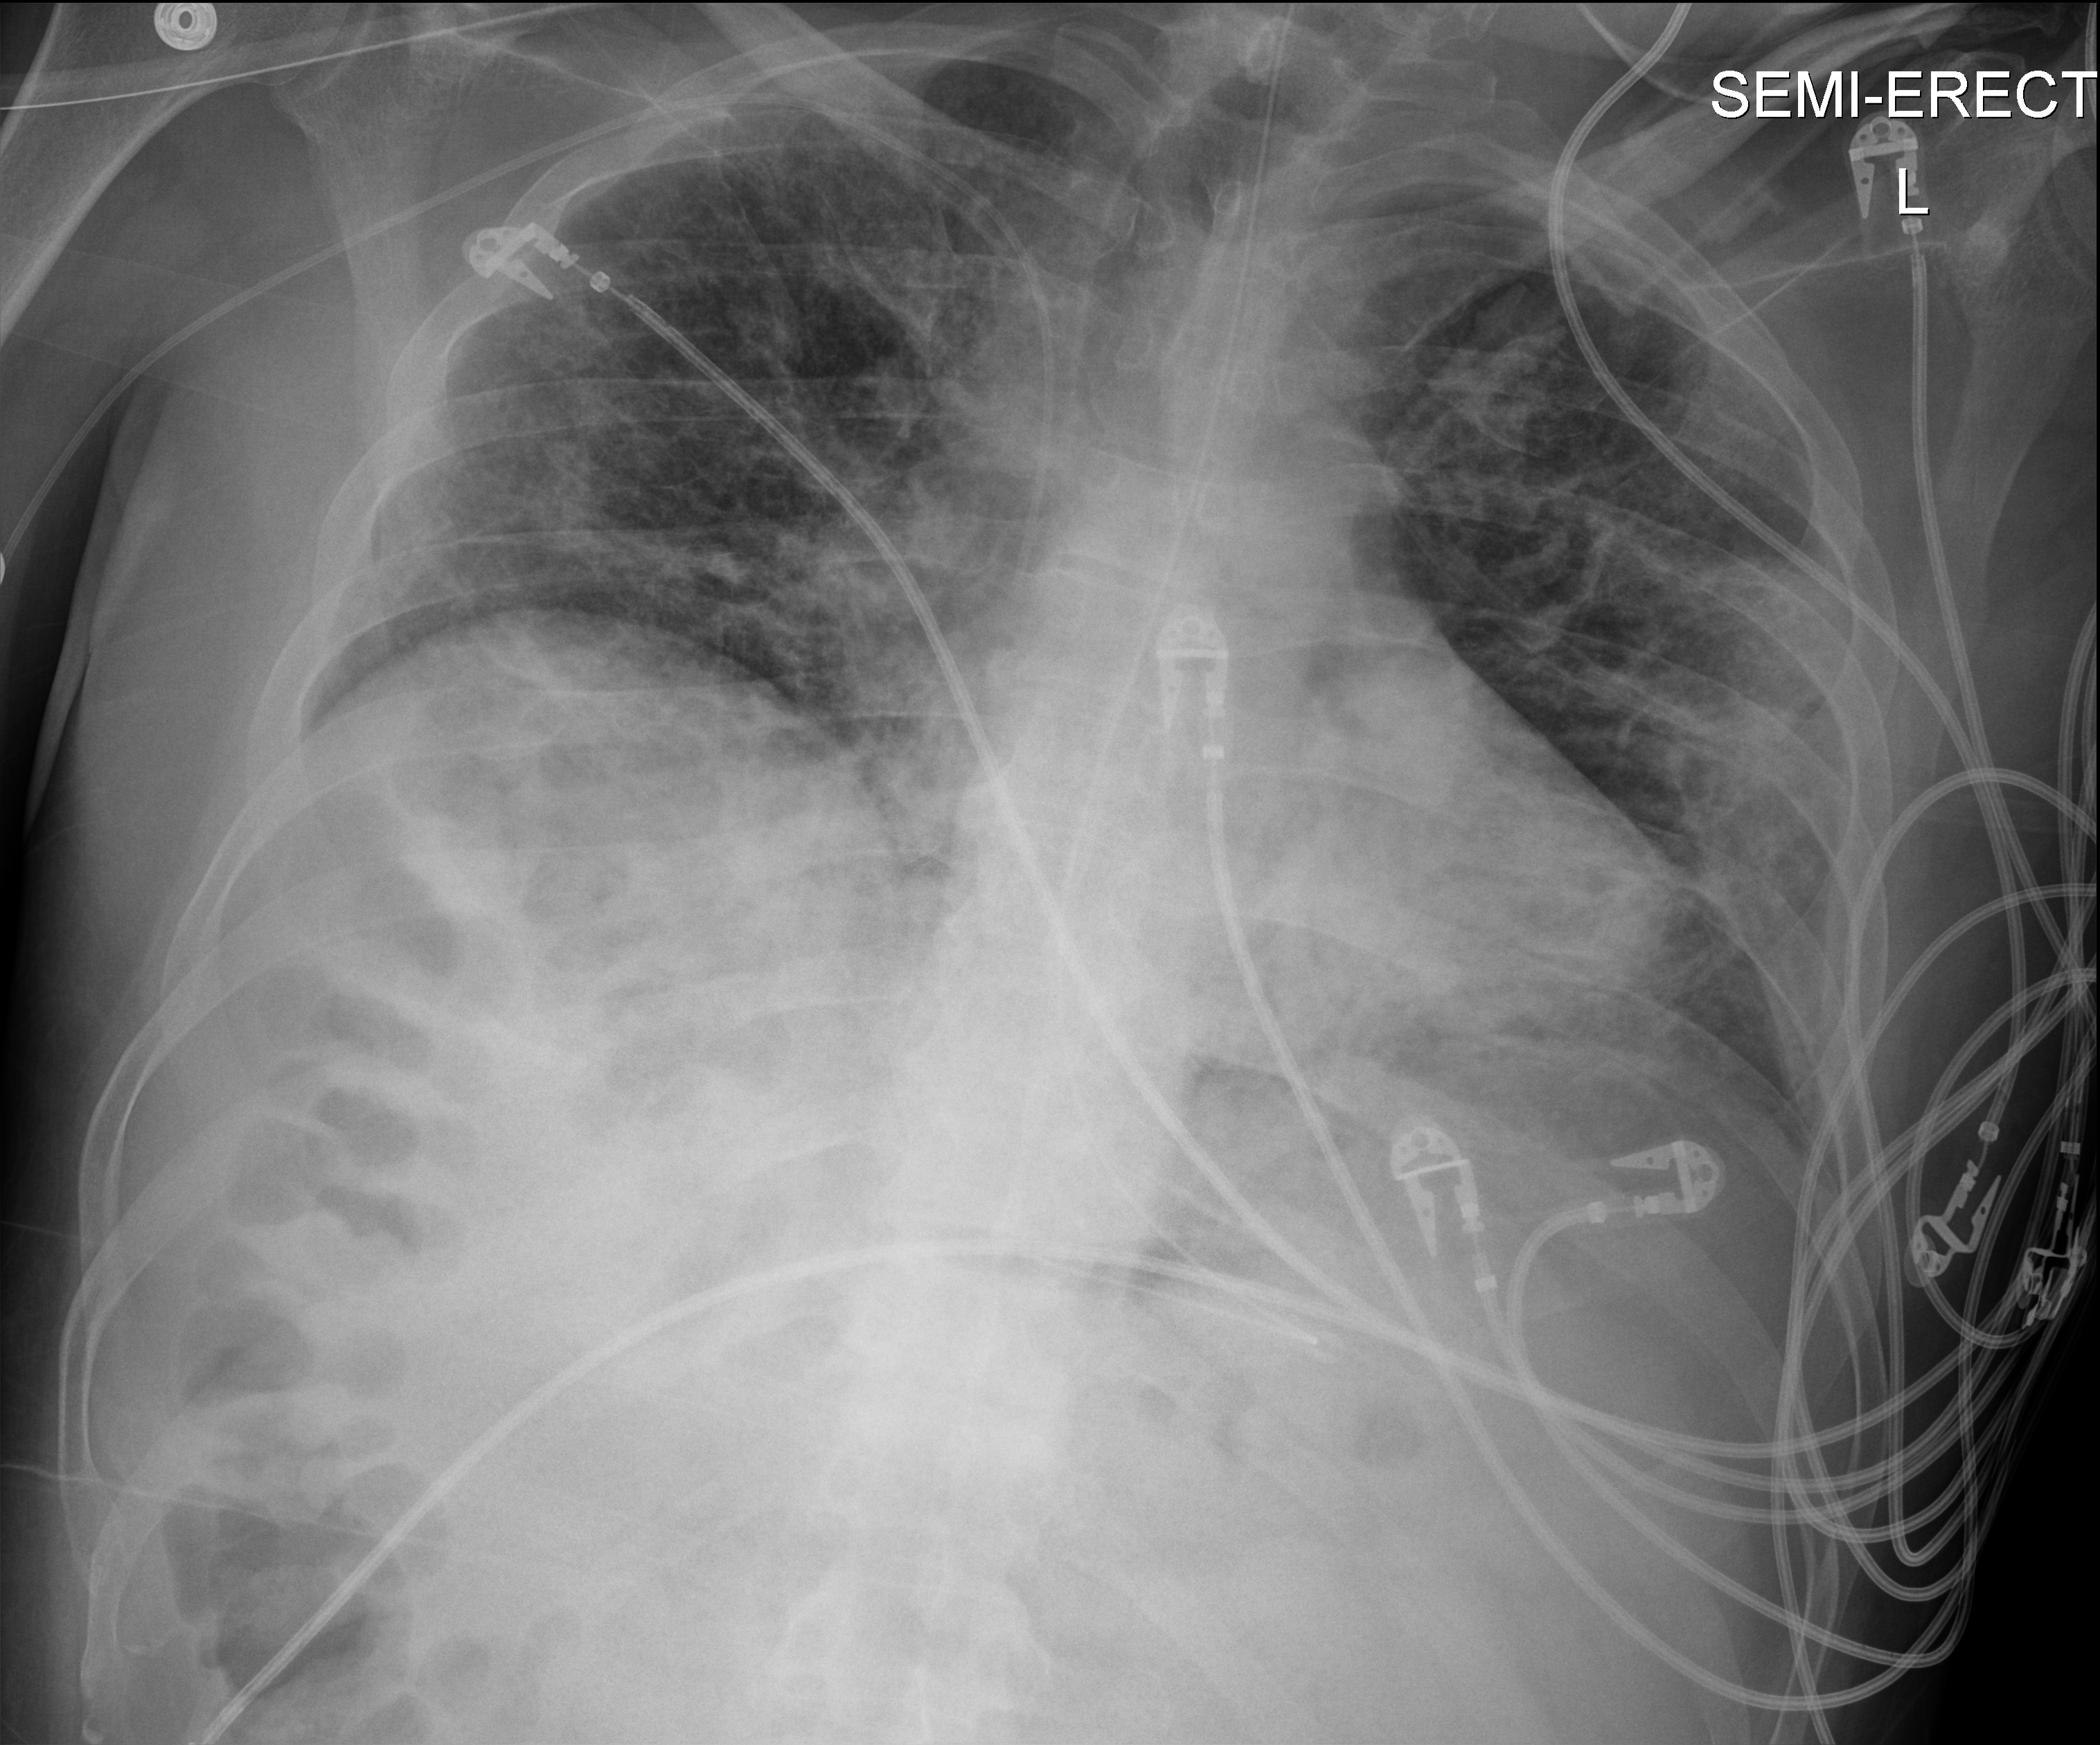
Portable chest radiograph; anteroposterior (AP) projection. Patient hospitalised with COVID-19; male, aged 18–59 years.
From the hospital-stay record, not from the radiograph (when in the stay this image was taken is not recorded): admitted to intensive care during this hospital stay: yes; other chronic lung disease (admission record): no.